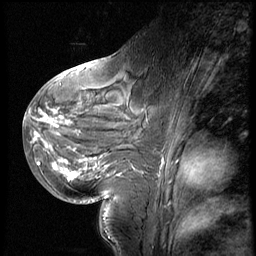
Breast MRI (dynamic contrast-enhanced), one sagittal slice. Position 27 of 60 along the scan axis. 3 images stored at this slice position (order not interpretable as contrast timing). 1.5 T. TE 4.2 ms, TR 8.9 ms. 2.5 mm slice thickness. 256 × 256 image matrix, field of view 200 × 200 mm. Female patient, age 29 years. From the clinical record (not read from this slice): setting: breast cancer imaged before/during neoadjuvant chemotherapy.
Structures marked on this image (semi-automatic segmentation, software-assisted and operator-edited):
- analysis volume of interest (the breast-tissue region the enhancement analysis was run in; not a lesion): box from (x=29, y=57) to (x=160, y=200) px
- tumour enhancement mask (voxels above the 140 % enhancement threshold inside the analysis volume of interest): (x=32, y=69)–(x=104, y=181)